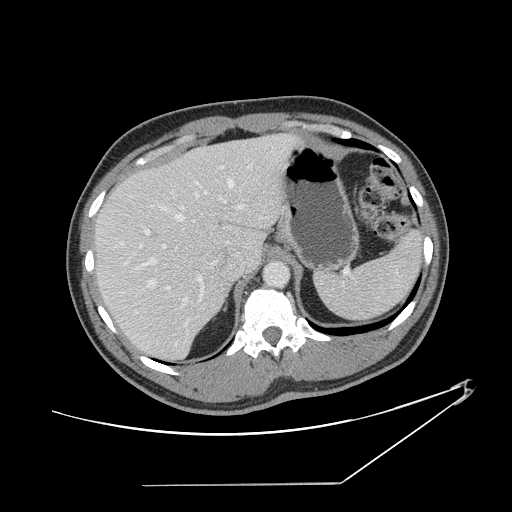
Contrast-enhanced abdominal CT, one axial slice; position 105 of 152 along the scan axis; reconstruction kernel STANDARD; soft-tissue window (W 400 / L 40 HU); 512 × 512 image matrix. Male patient, age 45 years. From the clinical record (not read from this slice): diagnosis: colorectal cancer liver metastases, imaged before liver resection; multiple liver metastases: no; largest metastasis: 1 cm.
Structures marked on this image (manually delineated by an expert):
- hepatic veins: bounding box <111,164,253,308> (left, top, right, bottom; pixels)
- liver: <96,135,295,361>
- planned liver remnant (the part of the liver to remain after resection): <96,154,234,361>
- portal vein (with intrahepatic branches): <140,182,243,327>